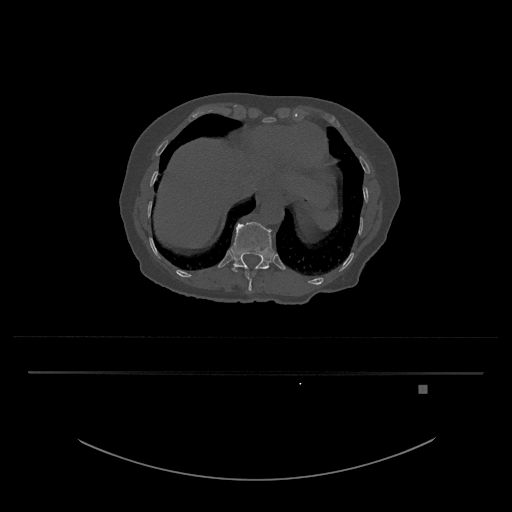
CT including the spine, one axial slice. 120 kVp. Bone window (W 1800 / L 400 HU). 512 × 512 image matrix, field of view 500 × 500 mm. Patient: female, 57 years. From the clinical record (not read from this slice): primary cancer: cervical.
Structures marked on this image (semi-automatic segmentation, software-assisted and operator-edited):
- T11 vertebra: bounding box <245,268,260,291> (left, top, right, bottom; pixels)
- T12 vertebra: <231,222,274,273>